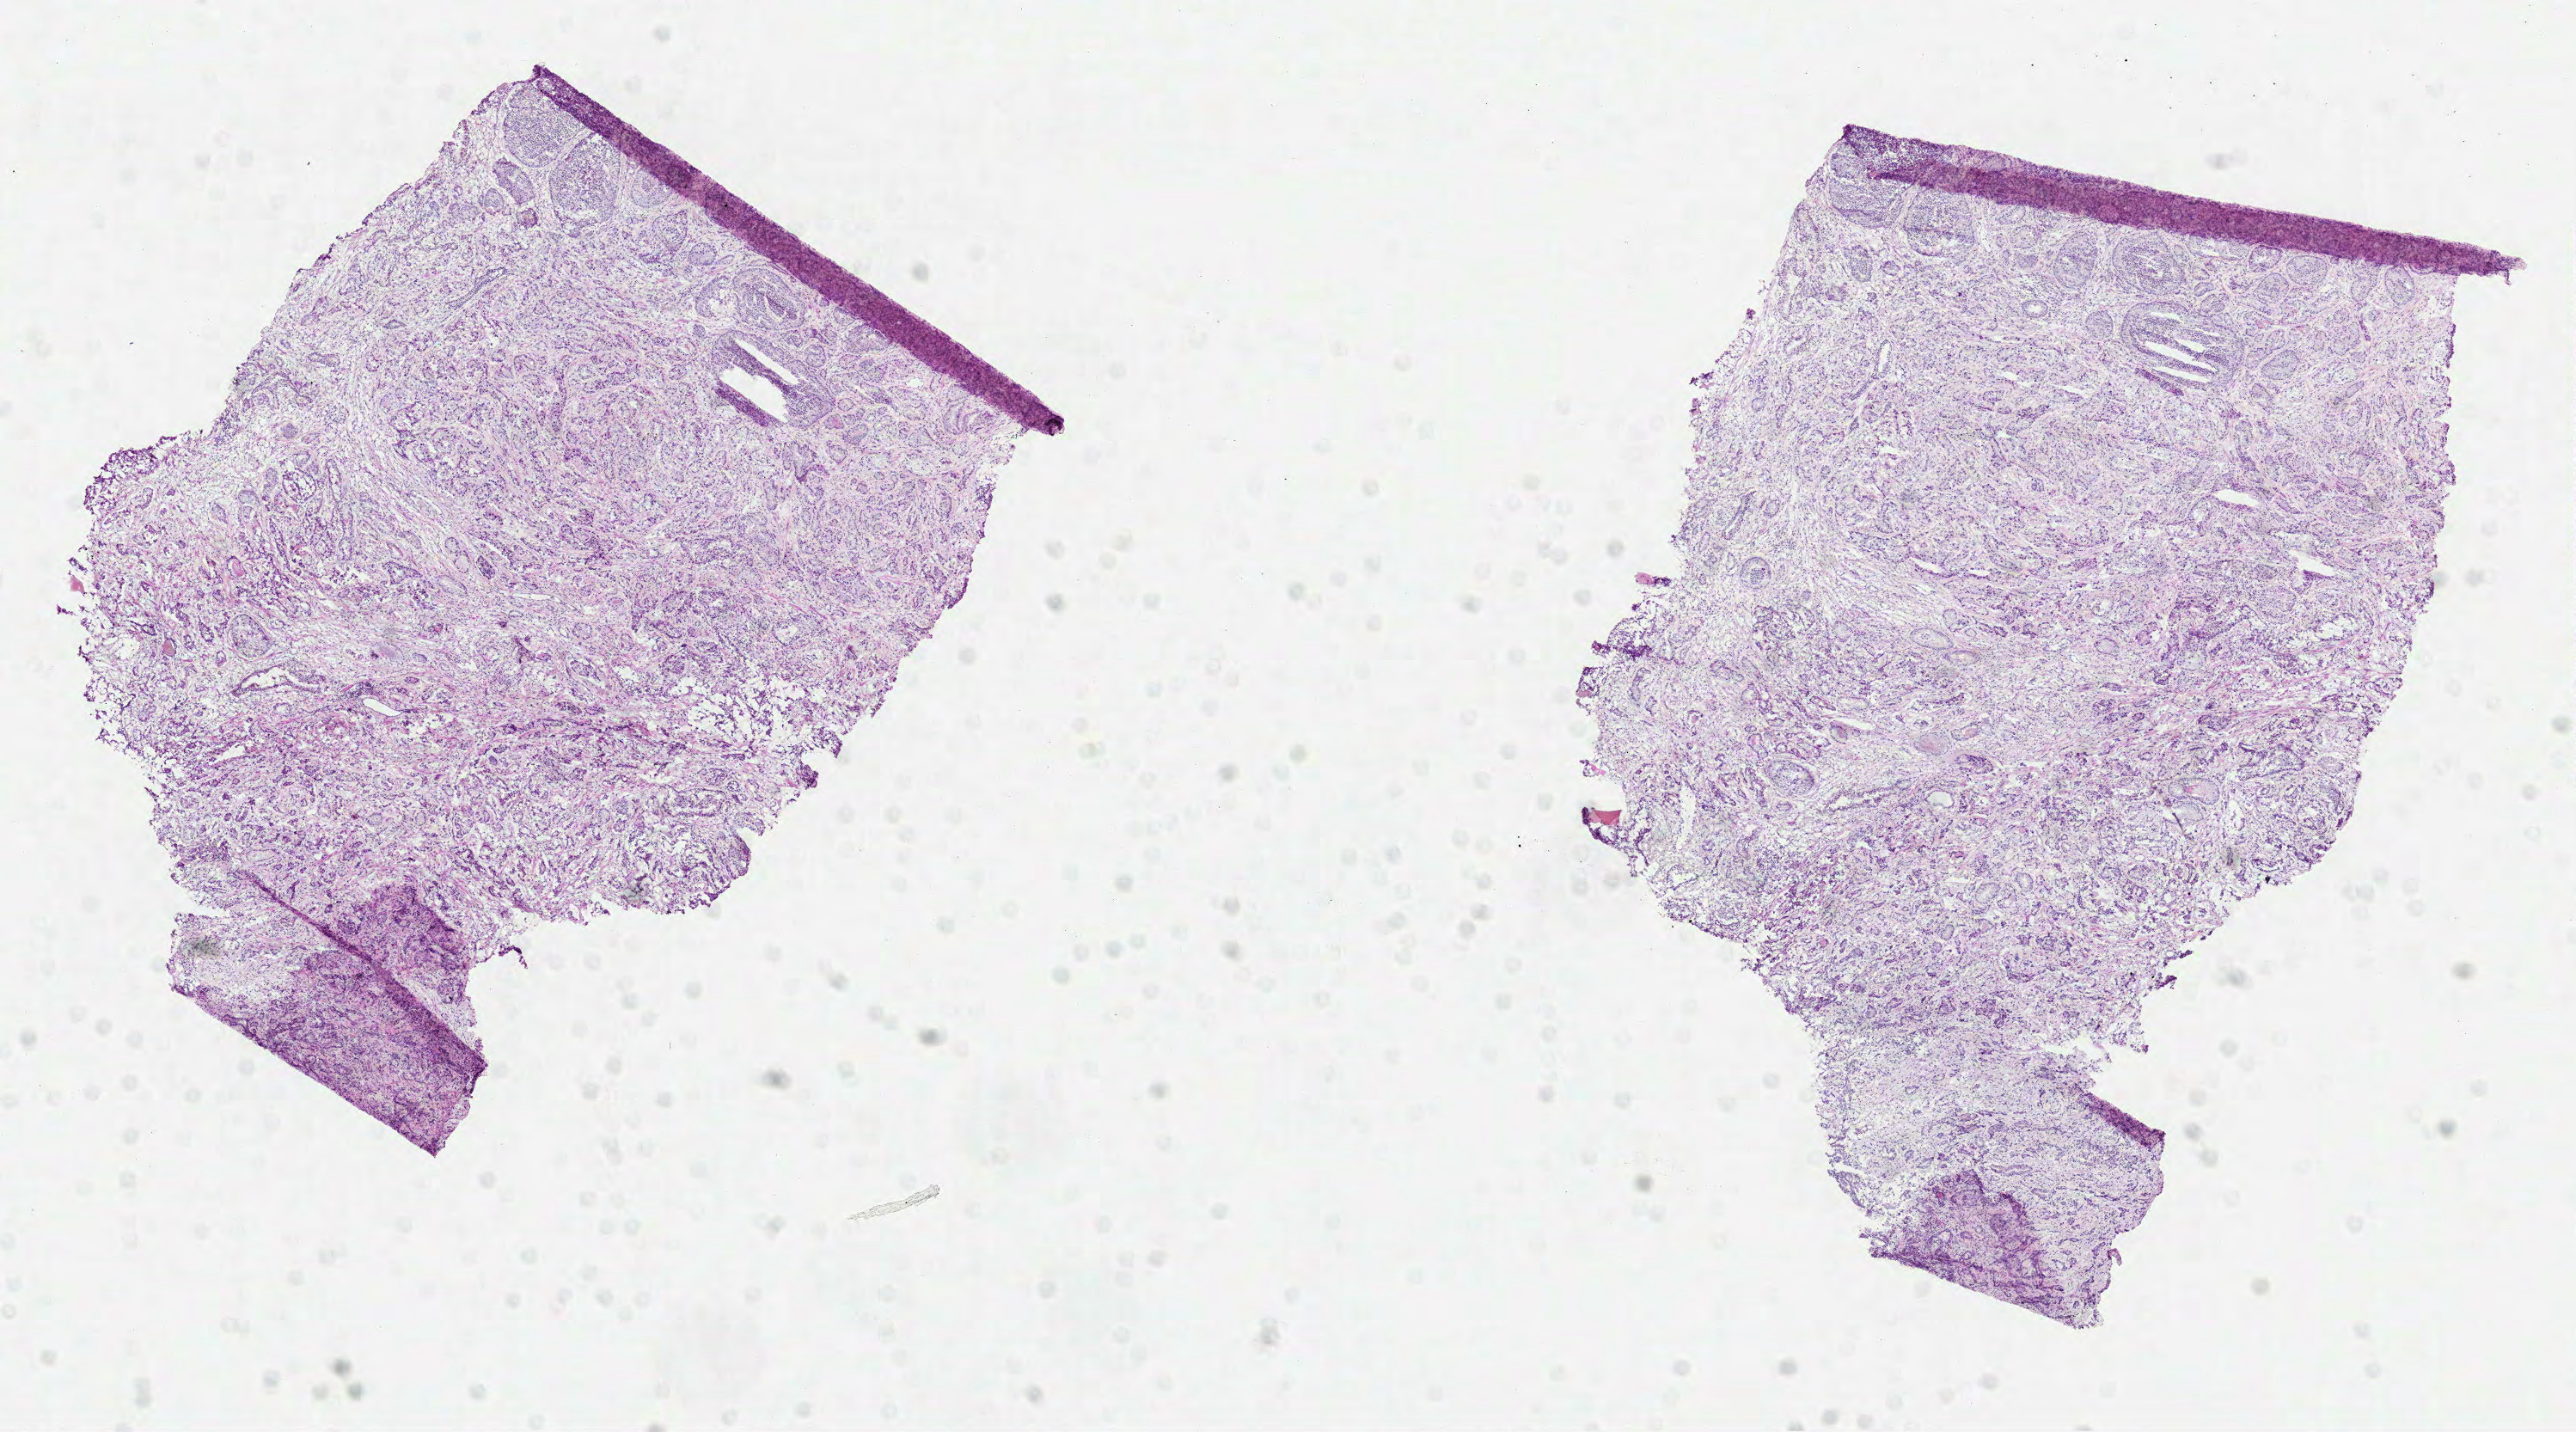
H&E-stained whole-slide image — low-resolution overview of the scanned area, about 12.1 x 6.7 mm (slide scanned at 40x). FFPE section. Sample: primary tumour, prostate. Male, age 72 years at initial diagnosis. Gleason score: 6 (2+4).
Diagnosis: Acinar cell carcinoma (prostate gland). Lymph nodes positive (case pathology): 0 of 16 examined. Laterality: bilateral.